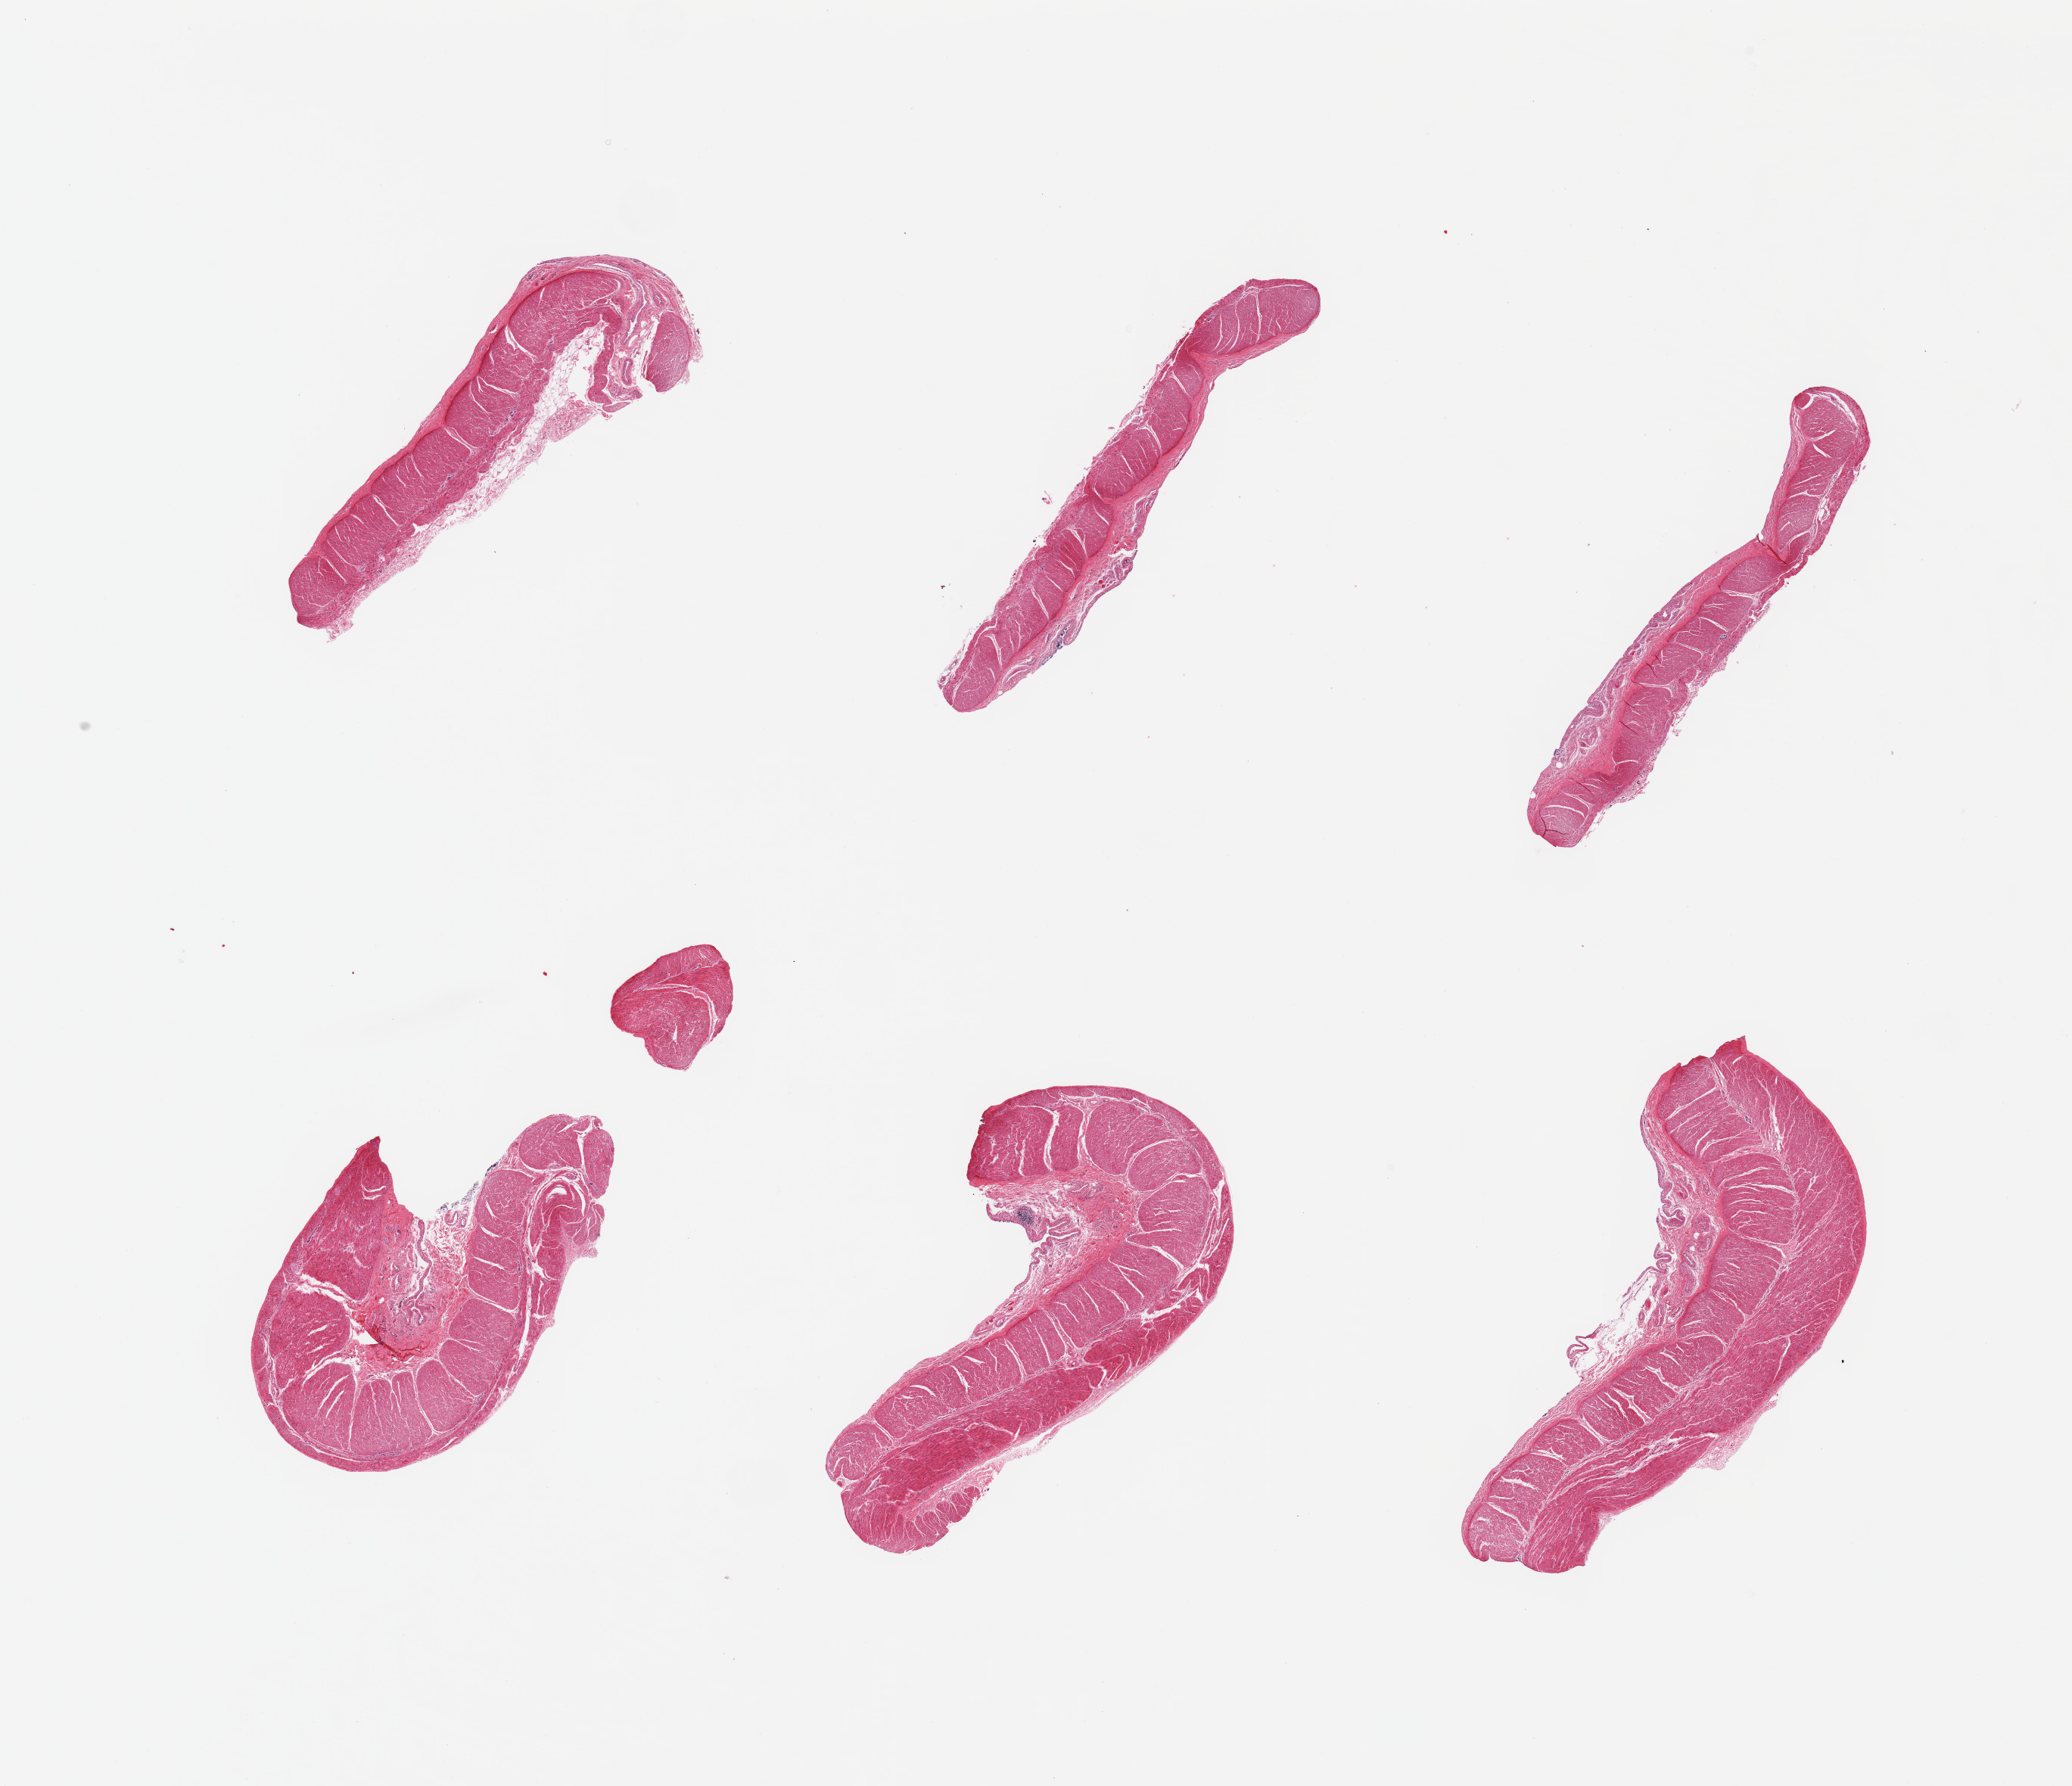
Whole-slide image, H&E stain, shown as a low-resolution overview of the whole scanned area (about 21.7 x 18.7 mm, slide scanned at 20x); PAXgene-fixed paraffin-embedded (PFPE) section; sampled site (target tissue): sigmoid colon; donor tissue sample.
Reviewer comment on this tissue sample: 6 pieces; well dissected muscularis.